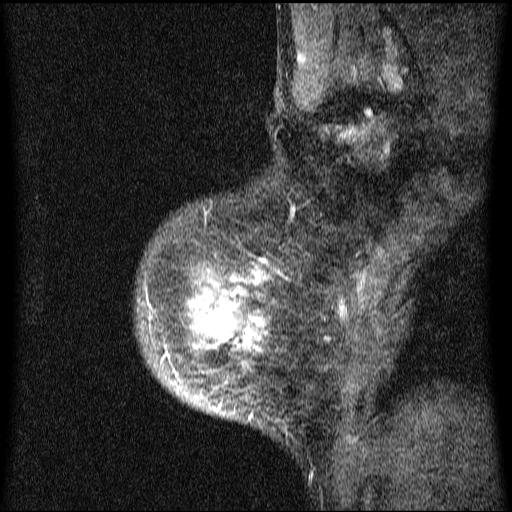
Breast MRI (dynamic contrast-enhanced), one sagittal slice; slice 54 of 64 in the series (ordered by position); dynamic contrast-enhanced series, image 2 of 4 at this slice position (ordered by acquisition); 1.5 T; TE 4.2 ms, TR 9.1 ms; 2 mm slice thickness; 512 × 512 image matrix, field of view 180 × 180 mm. Female patient, age 33 years.
Structures marked on this image (semi-automatic segmentation, software-assisted and operator-edited):
- analysis volume of interest (the breast-tissue region the enhancement analysis was run in; not a lesion): bounding box [x1, y1, x2, y2] px = [138, 156, 331, 434]
- tumour enhancement mask (voxels above the 70 % enhancement threshold inside the analysis volume of interest): [148, 259, 270, 423]